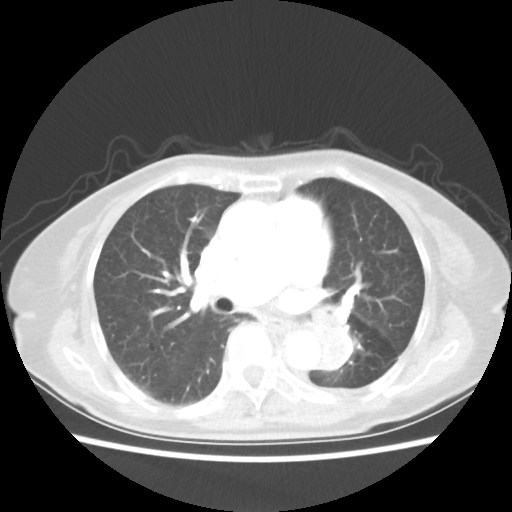
Chest CT, one axial slice. Slice 27 of 50 in the series (ordered by position). 80 kVp. Lung window (W 1500 / L -600 HU). 512 × 512 image matrix. Patient: female, 81 years. From the clinical record (not read from this slice): clinical TNM (as recorded): T2 N0 M1a.
Outlined on this slice (rectangle marked by the reading radiologist):
- lung tumour (recorded histology: squamous cell carcinoma): bounding box [x1, y1, x2, y2] px = [307, 319, 360, 380]